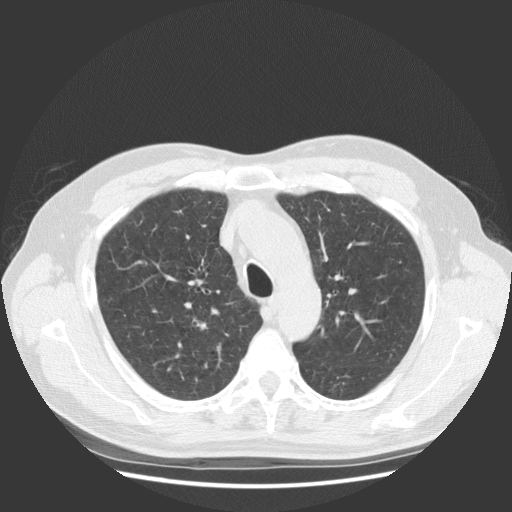
Low-dose screening chest CT, one axial slice; position 95 of 131 along the scan axis; 140 kVp; lung window (W 1500 / L -600 HU); 2.5 mm slice thickness; 512 × 512 image matrix, field of view 369 × 369 mm.
Outlined on this slice (outlined manually by an expert reader):
- lesion 1 (tumor, upper lobe of right lung): box from (x=193, y=319) to (x=207, y=330) px